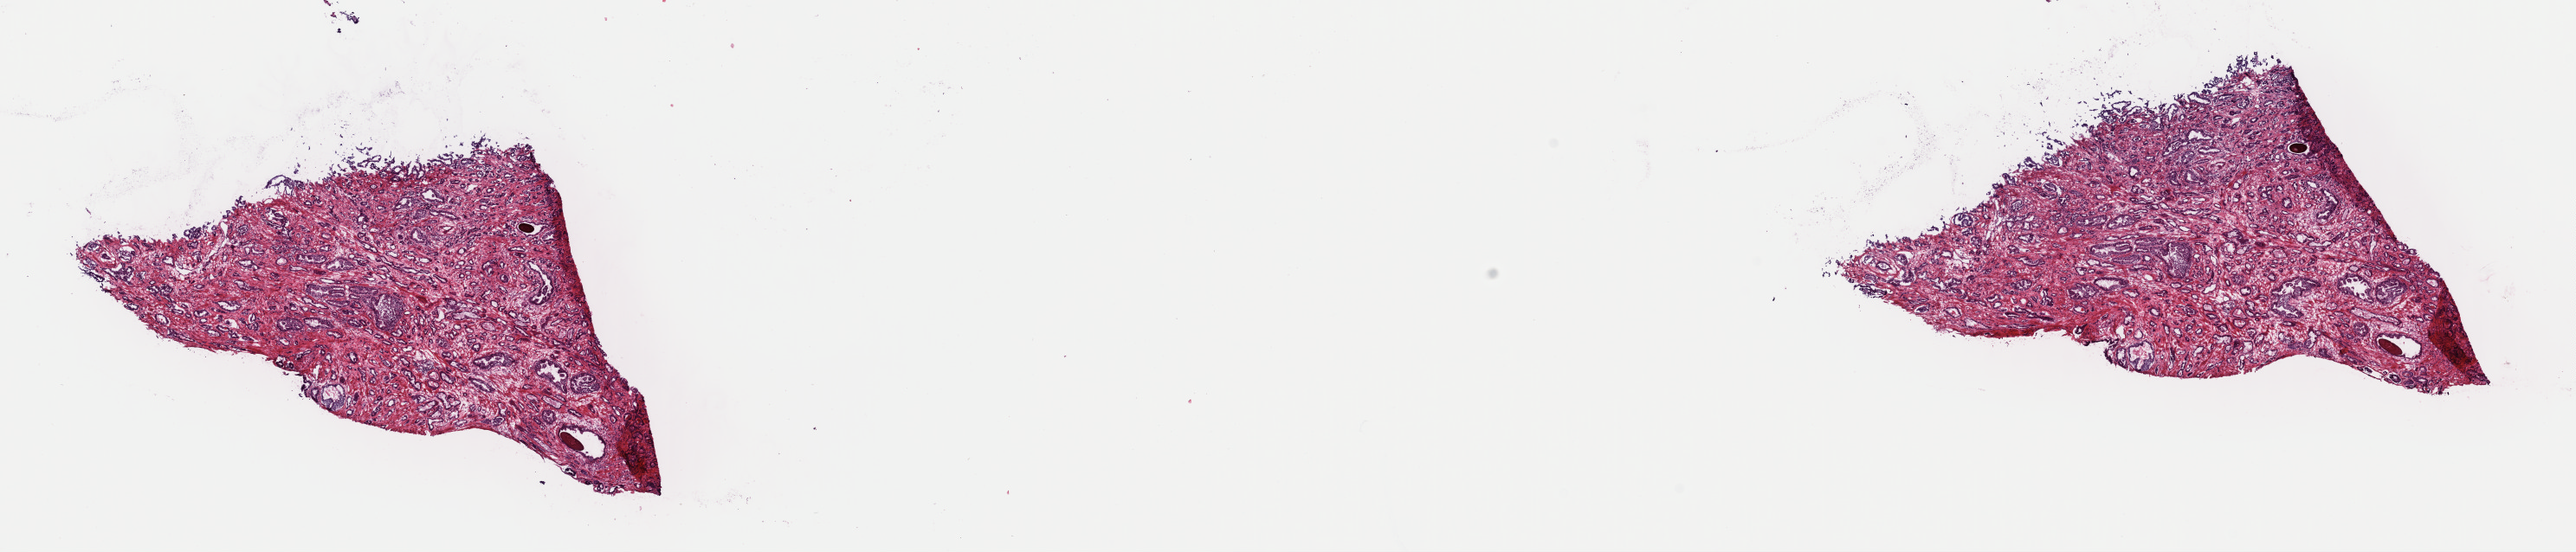
H&E whole-slide image — shown as a low-resolution overview of the whole scanned area (about 23.5 x 5.0 mm, slide scanned at 40x); frozen section; prostate, primary tumour sample. Male patient; age at initial diagnosis 51 years. Gleason score: 7 (4+3). Pathologist review of this section (percent, as recorded): tumour cells 40%, tumour nuclei 60%, normal cells 20%, stromal cells 40%, necrosis 0%. Infiltration values recorded for this section: lymphocyte infiltration 0%, monocyte infiltration 0%, neutrophil infiltration 0%.
Histologic diagnosis: Acinar cell carcinoma (prostate gland).